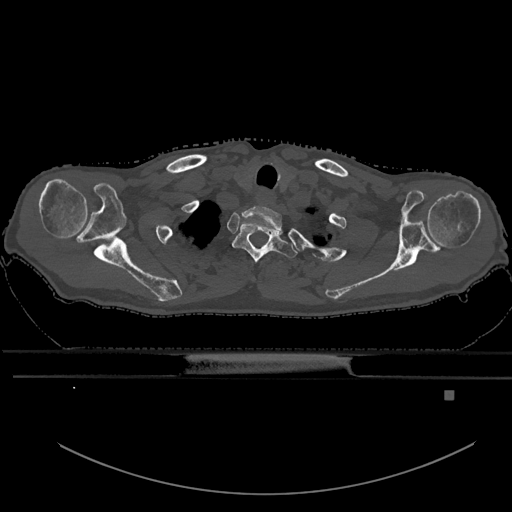
CT including the spine, one axial slice. Slice 542 of 969 in the series (ordered by position). Bone window (W 1800 / L 400 HU). 0.5 mm slice thickness. 512 × 512 image matrix, field of view 456 × 456 mm. Patient: male, 82 years. Case-level facts recorded for this patient, not image findings: primary cancer: prostate; vertebrae with lytic lesions (as recorded): T11, T9, T8, T2.
Annotated regions visible in this slice (semi-automatic segmentation, software-assisted and operator-edited):
- T1 vertebra: bounding box (x1, y1, x2, y2) in pixels: (232, 222, 297, 264)